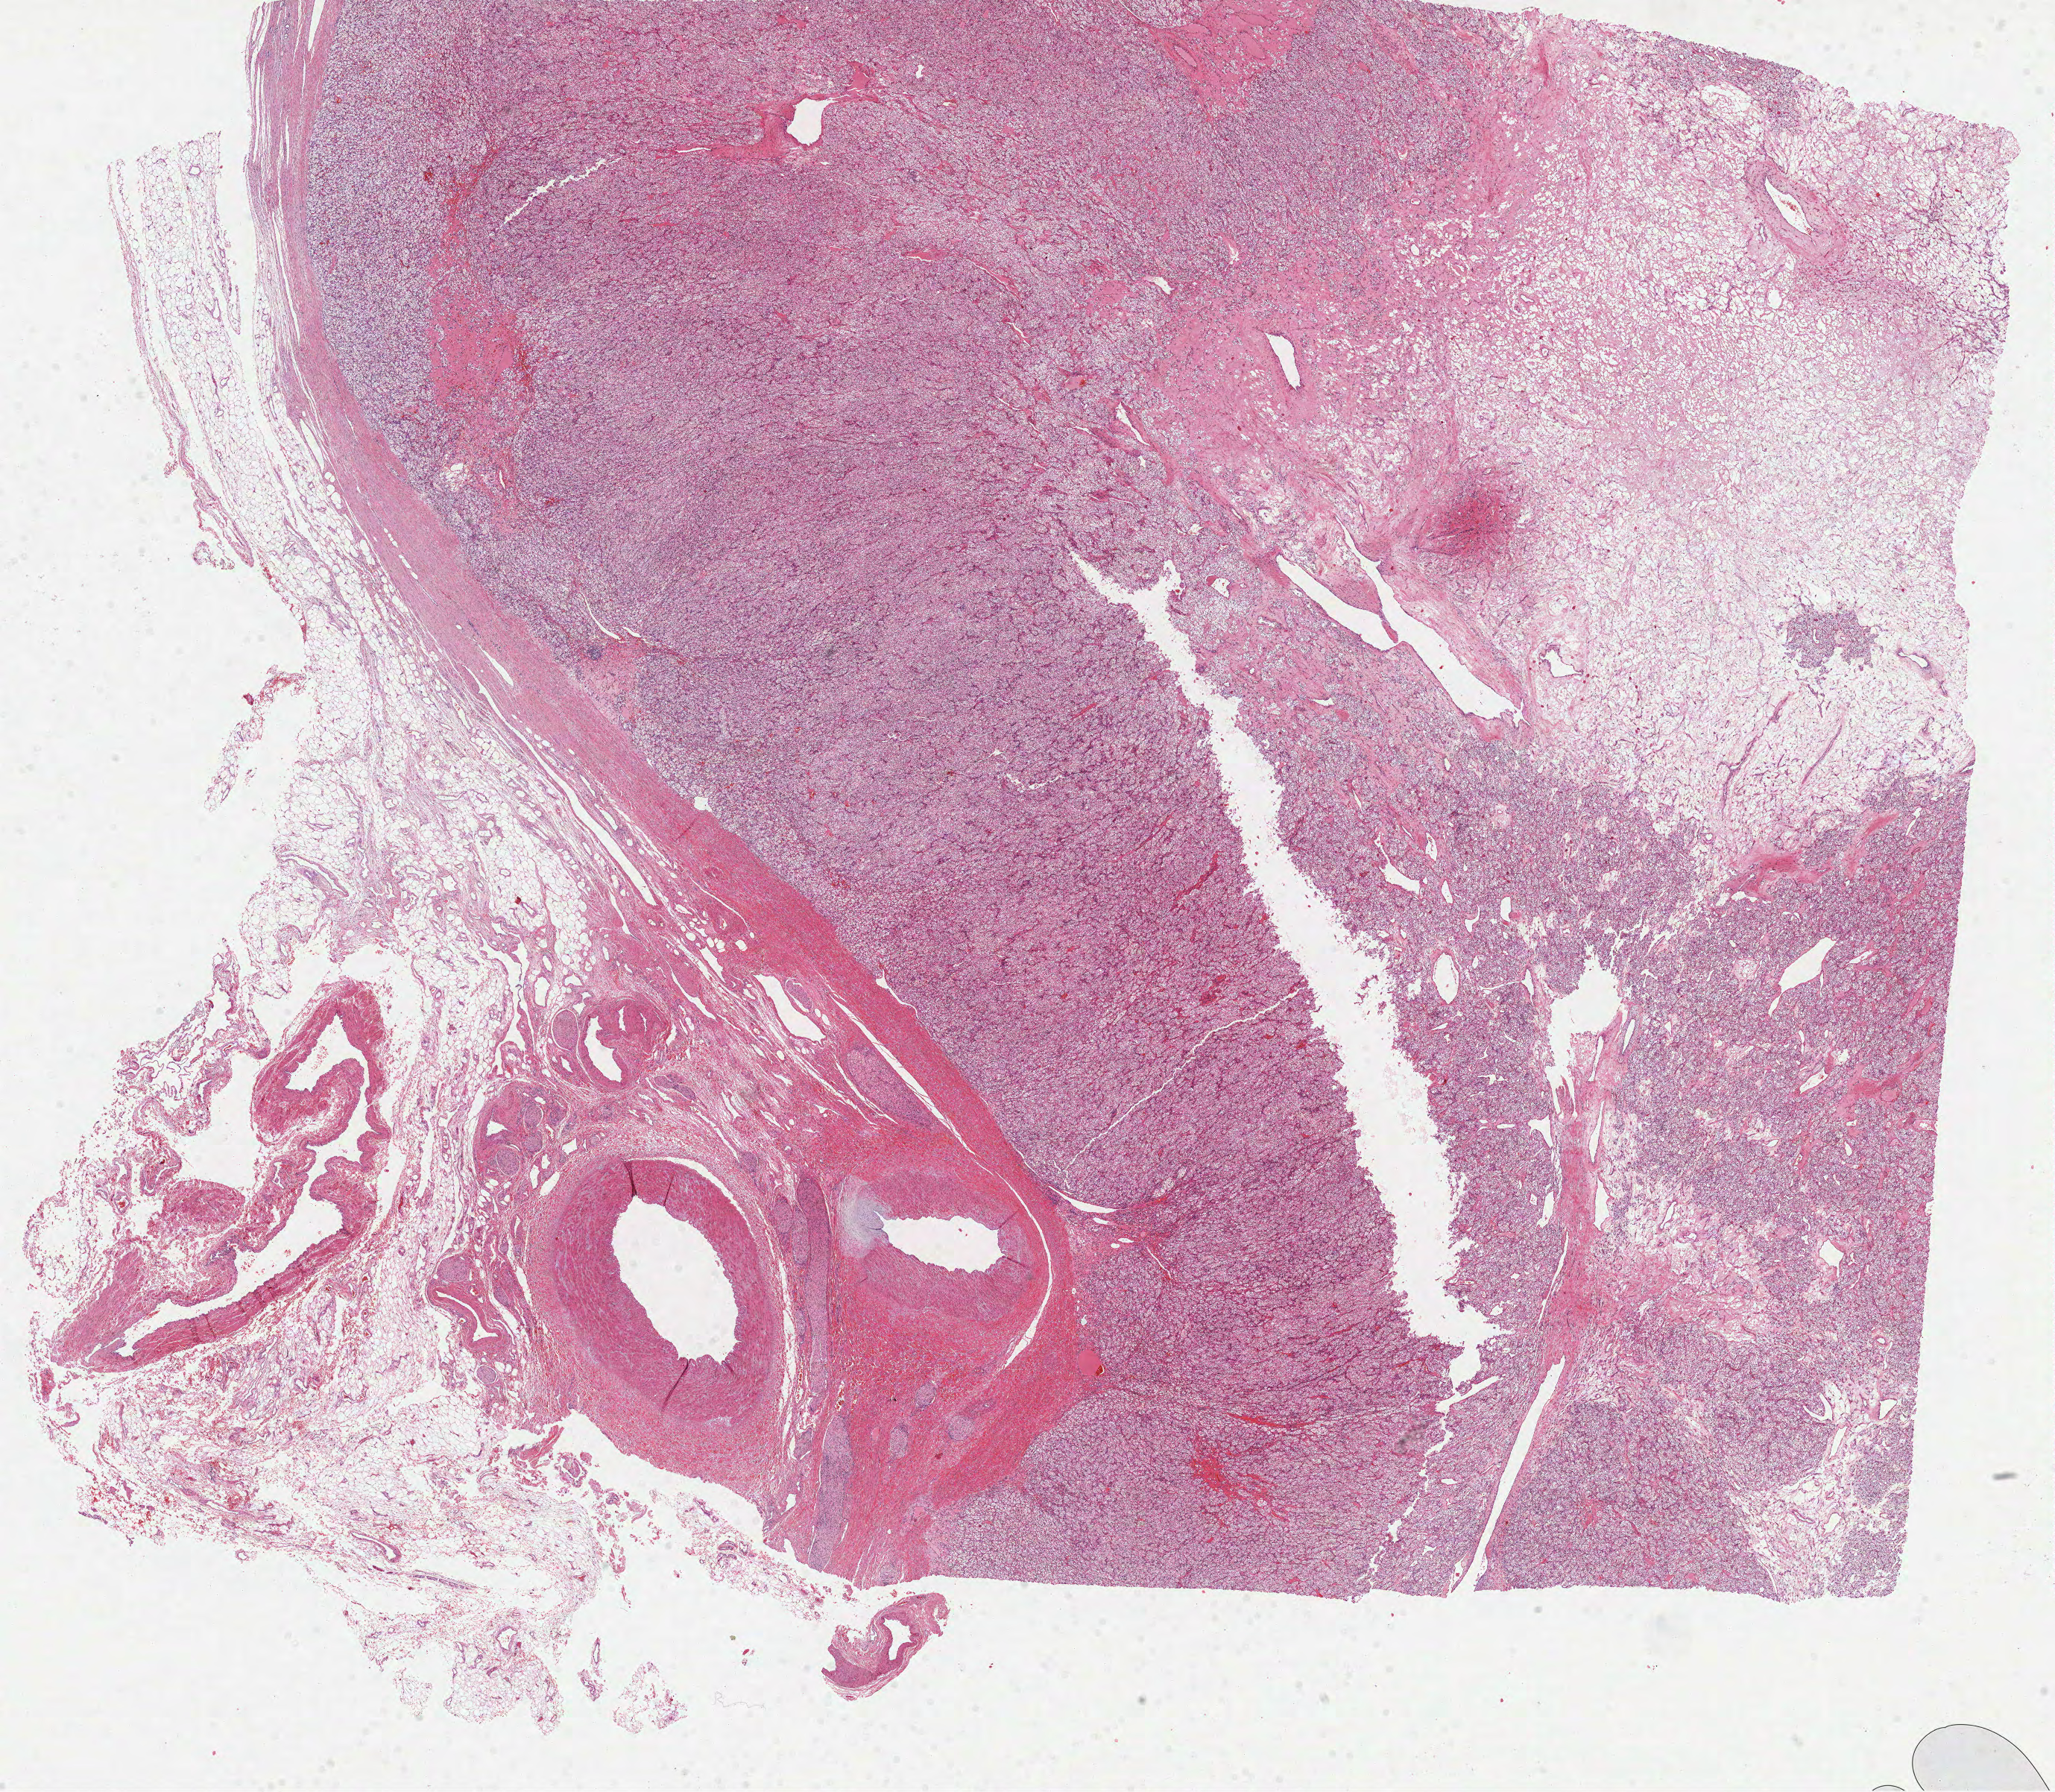
Digitized H&E tissue section (whole slide), low-resolution overview of the scanned area, about 22.2 x 19.4 mm; FFPE section; kidney, primary tumour sample. Male patient; age at initial diagnosis 50 years. Histologic grade: G3 (poorly differentiated).
Laterality: right. Diagnosis: Clear cell adenocarcinoma, NOS. AJCC pathologic stage: III (6th edition).